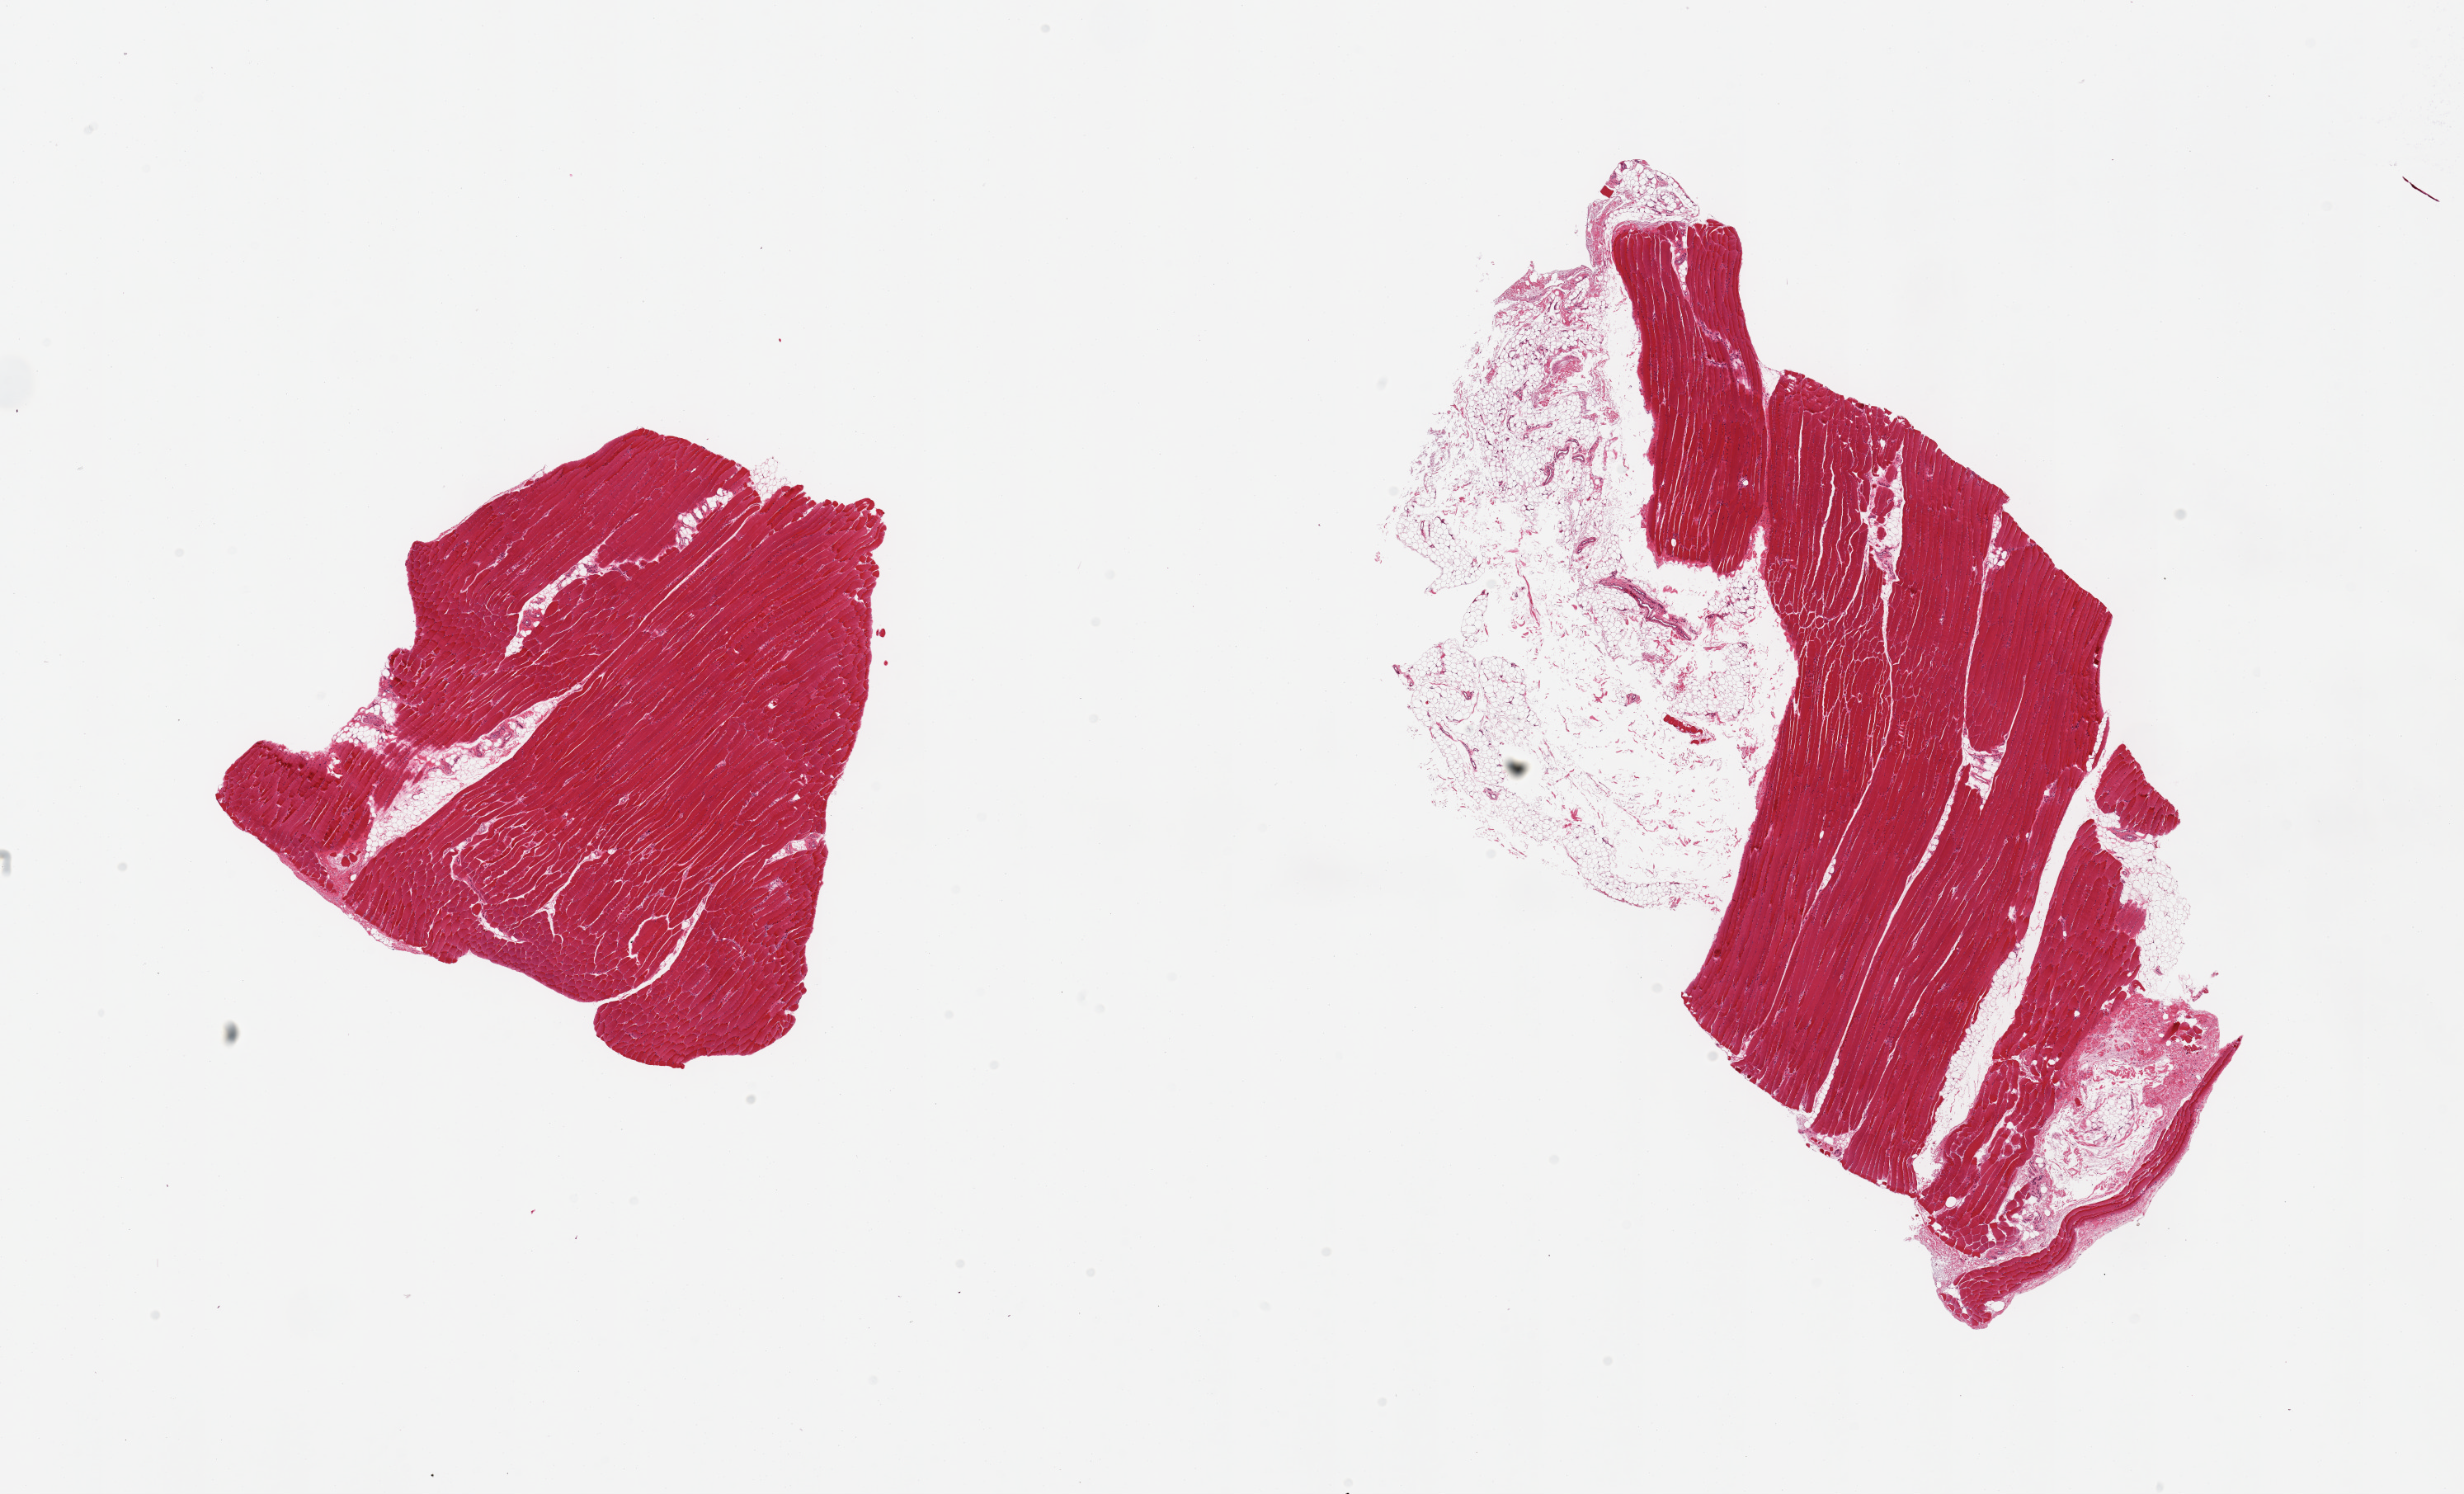
Hematoxylin and eosin (H&E) whole-slide image, whole scanned area (about 23.6 x 14.3 mm) shown as a low-resolution overview. PAXgene-fixed paraffin-embedded (PFPE) section. Target tissue: skeletal muscle. Tissue donor sample. Female donor.
Review note (as recorded): 2 pieces; one piece is 30% fat.